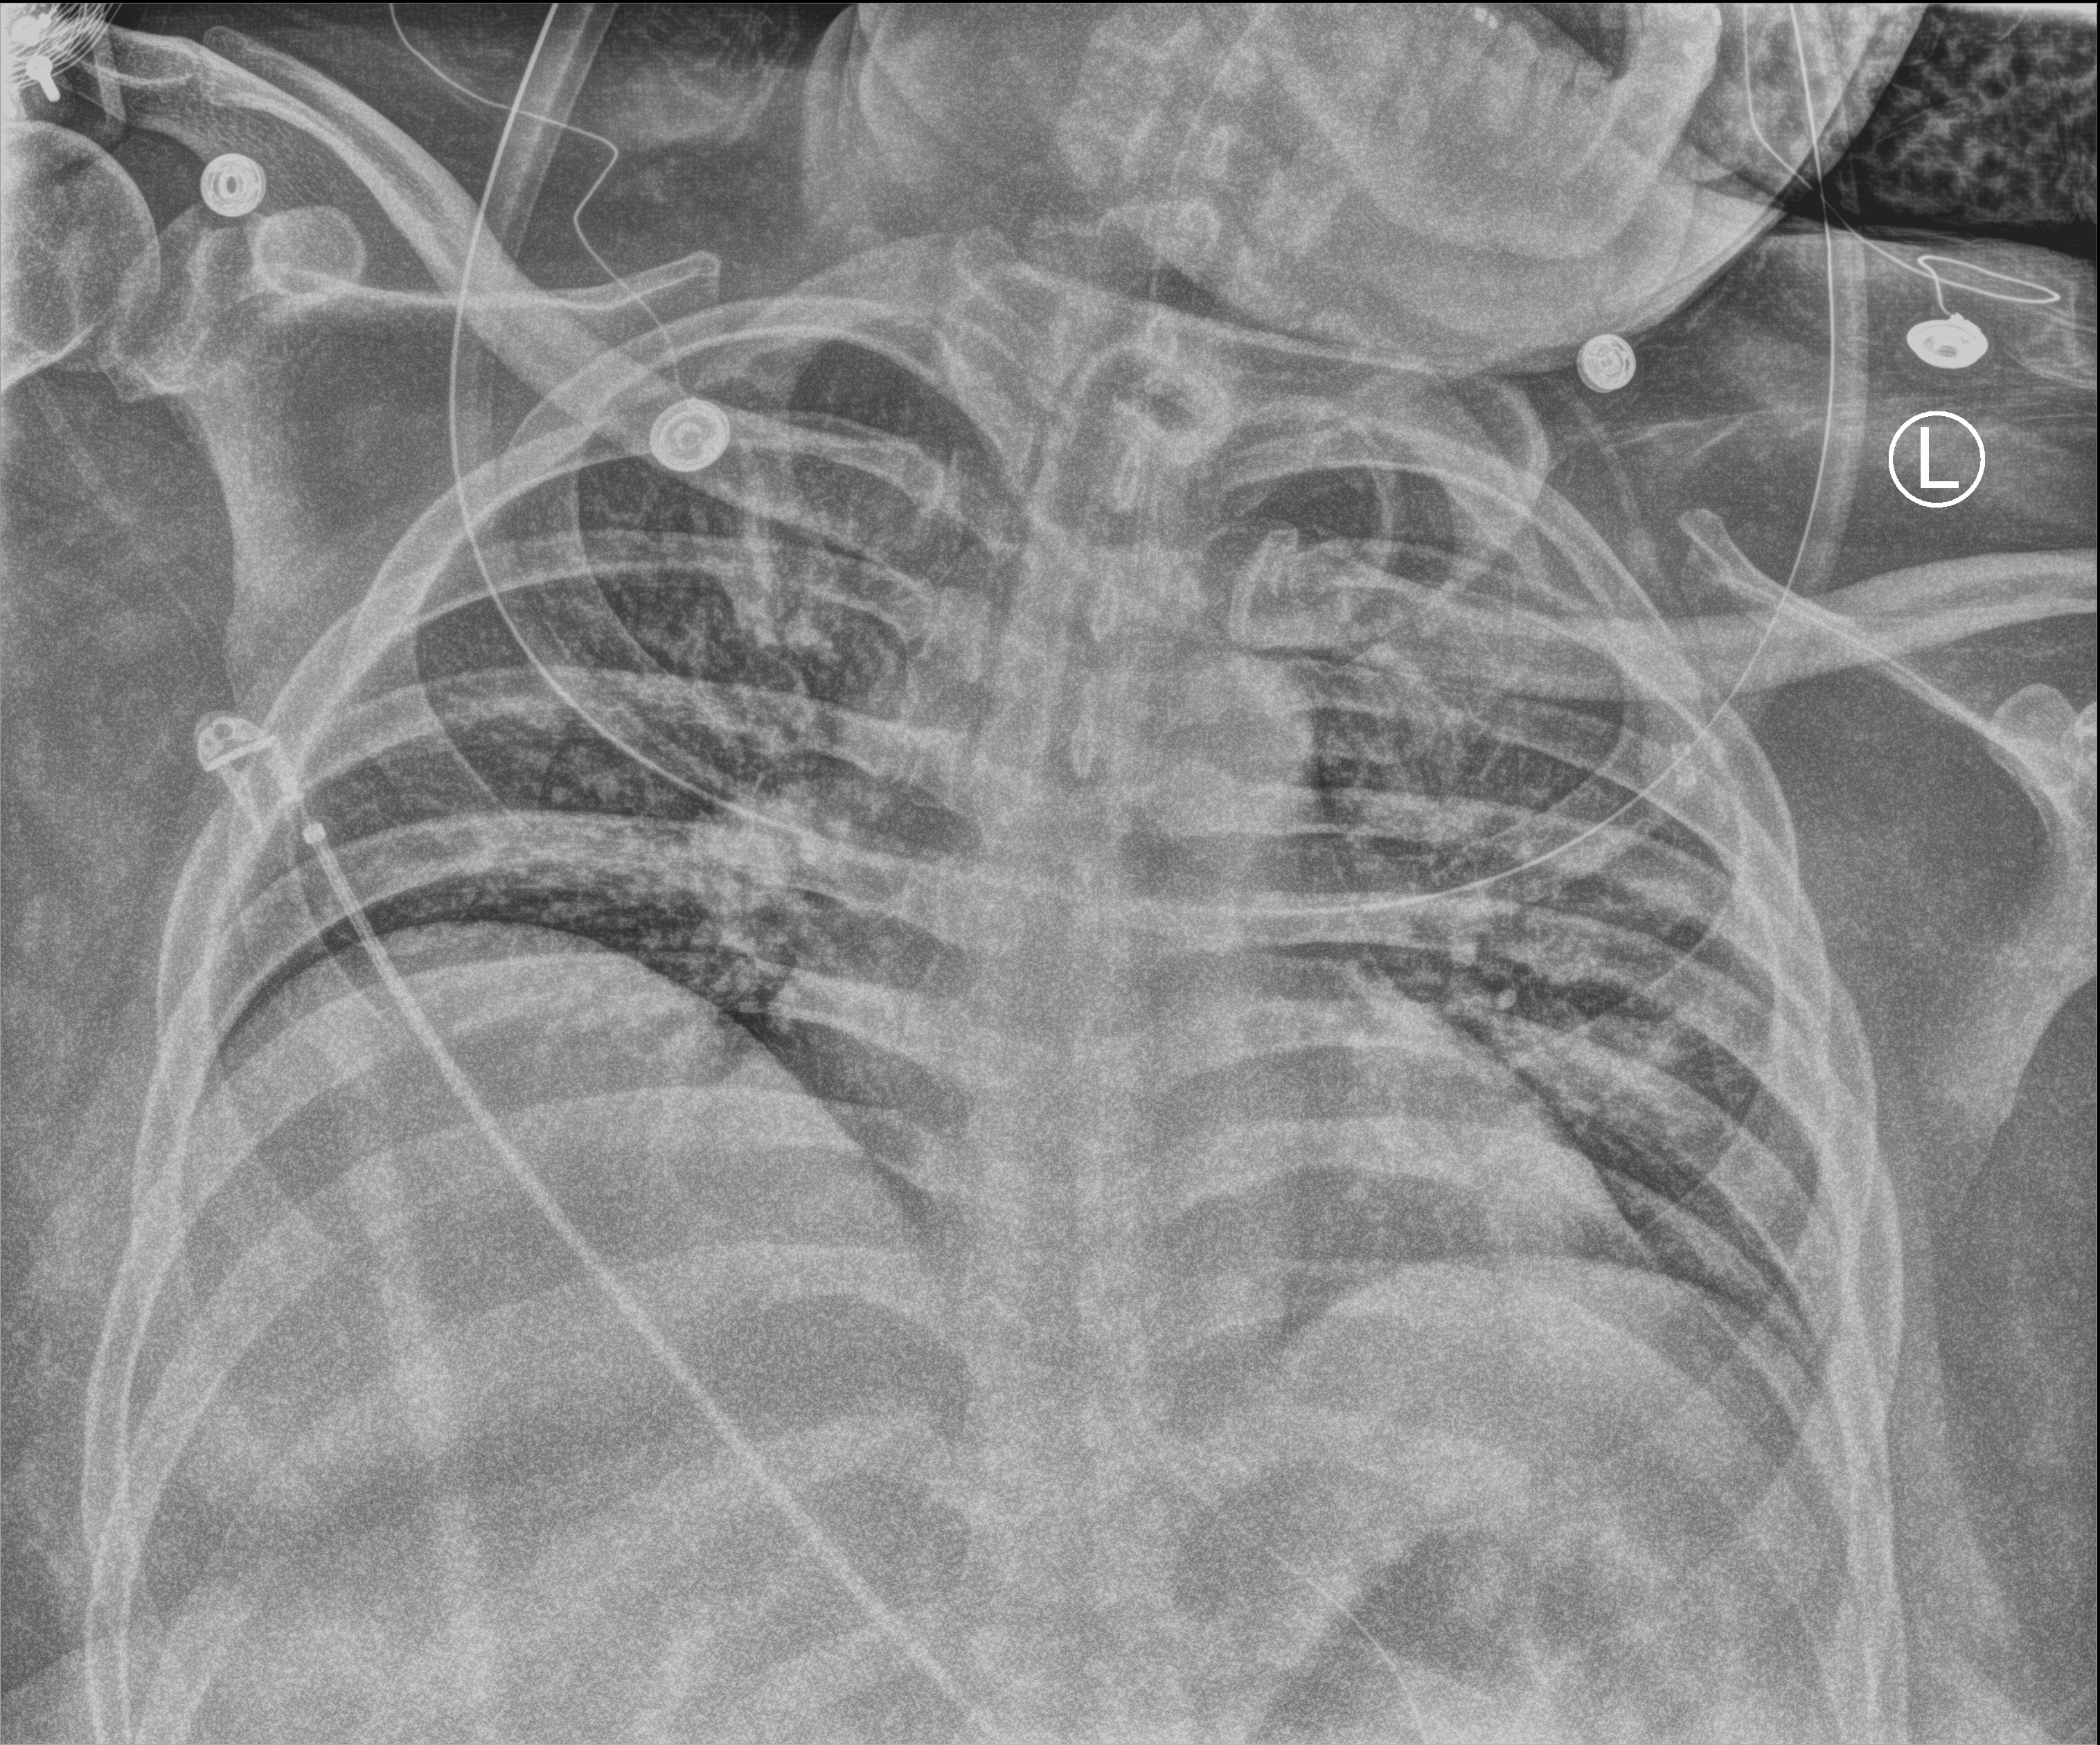
Chest X-ray (portable), anteroposterior (AP) projection. Patient hospitalised with COVID-19; male, aged 18–59 years.
From the hospital-stay record, not from the radiograph (when in the stay this image was taken is not recorded):
- admitted to intensive care during this hospital stay: yes
- mechanically ventilated during this hospital stay: yes
- other chronic lung disease (admission record): yes